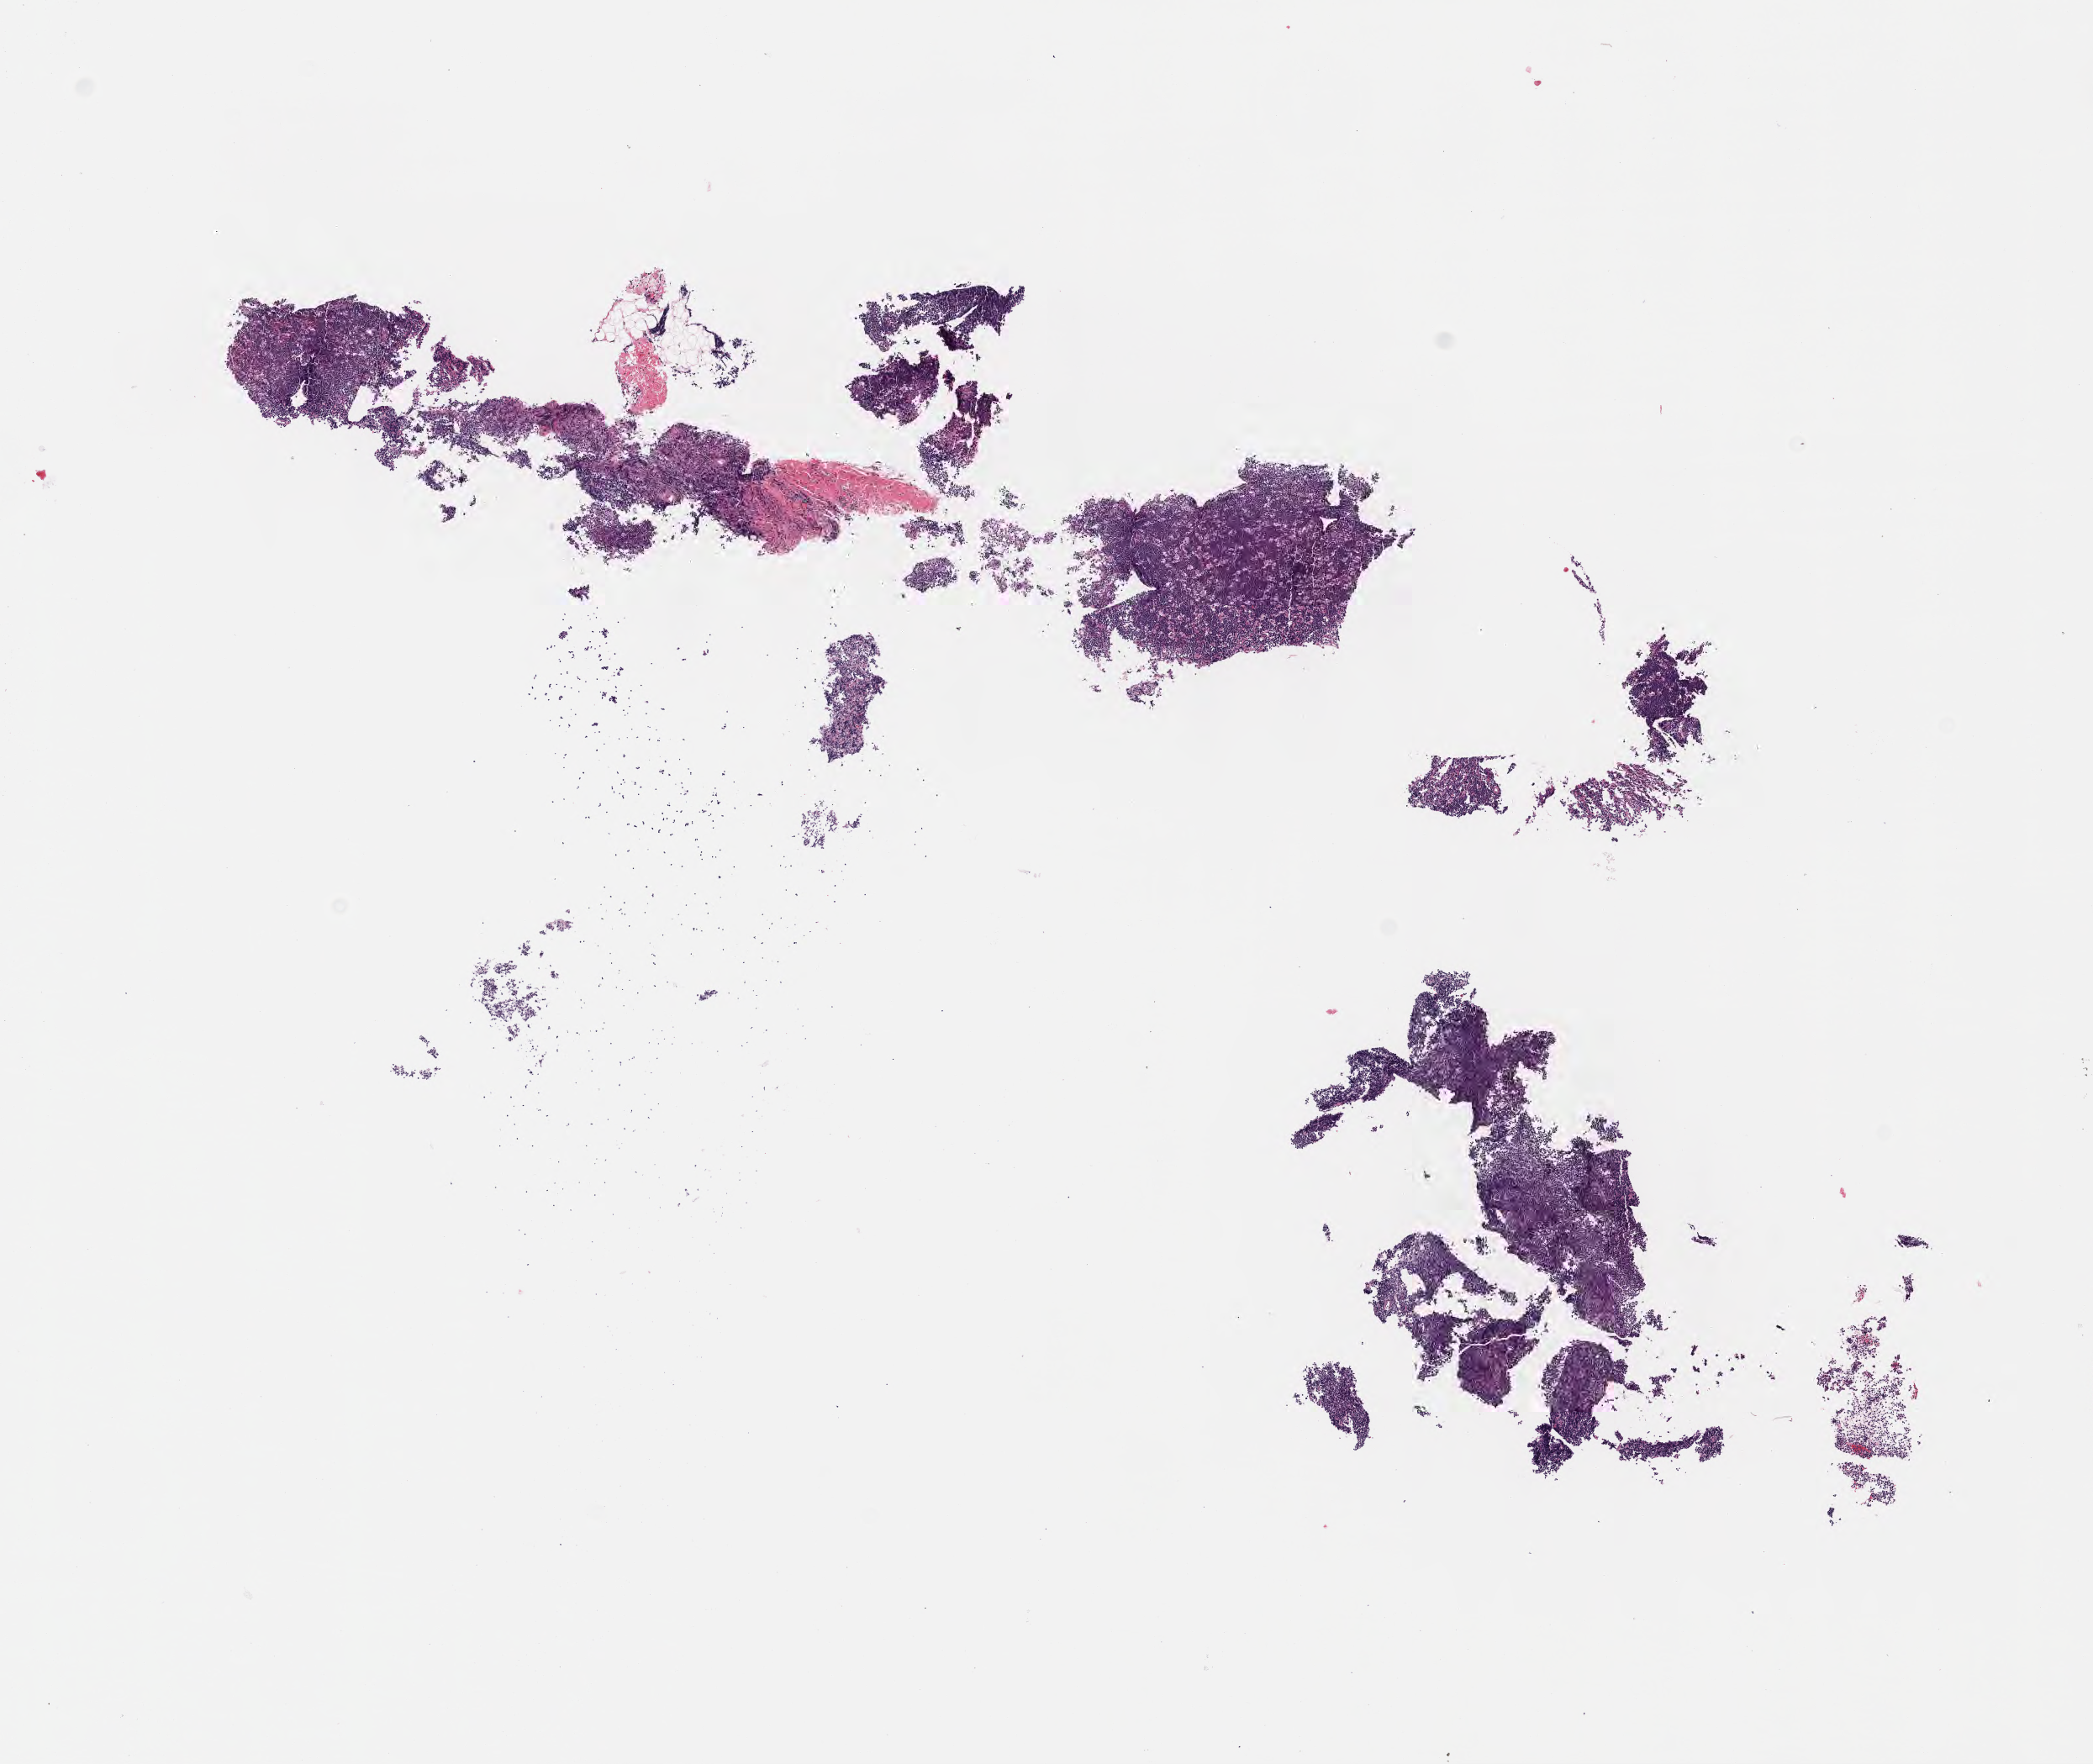
Digitized hematoxylin and eosin (H&E)-stained section — whole scanned area (about 10.1 x 8.5 mm) shown as a low-resolution overview; tumor tissue; anatomic site: cranium. Female patient; age at initial diagnosis 1 years.
Histologic diagnosis: Burkitt lymphoma, NOS.